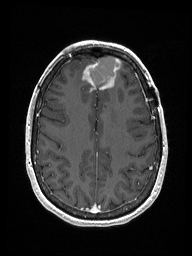
Brain MRI from a brain-tumour surgery series, one axial slice; position 57 of 192 along the scan axis; T1-weighted post-contrast; 1 mm slice thickness; 192 × 256 image matrix. Case-level facts recorded for this patient, not image findings: histopathology: Metastastic Carcinoma from Breast primary; tumour location: Right Frontal.
Outlined on this slice (manually delineated by an expert):
- previous resection cavity: bounding box [x1, y1, x2, y2] px = [90, 56, 119, 86]